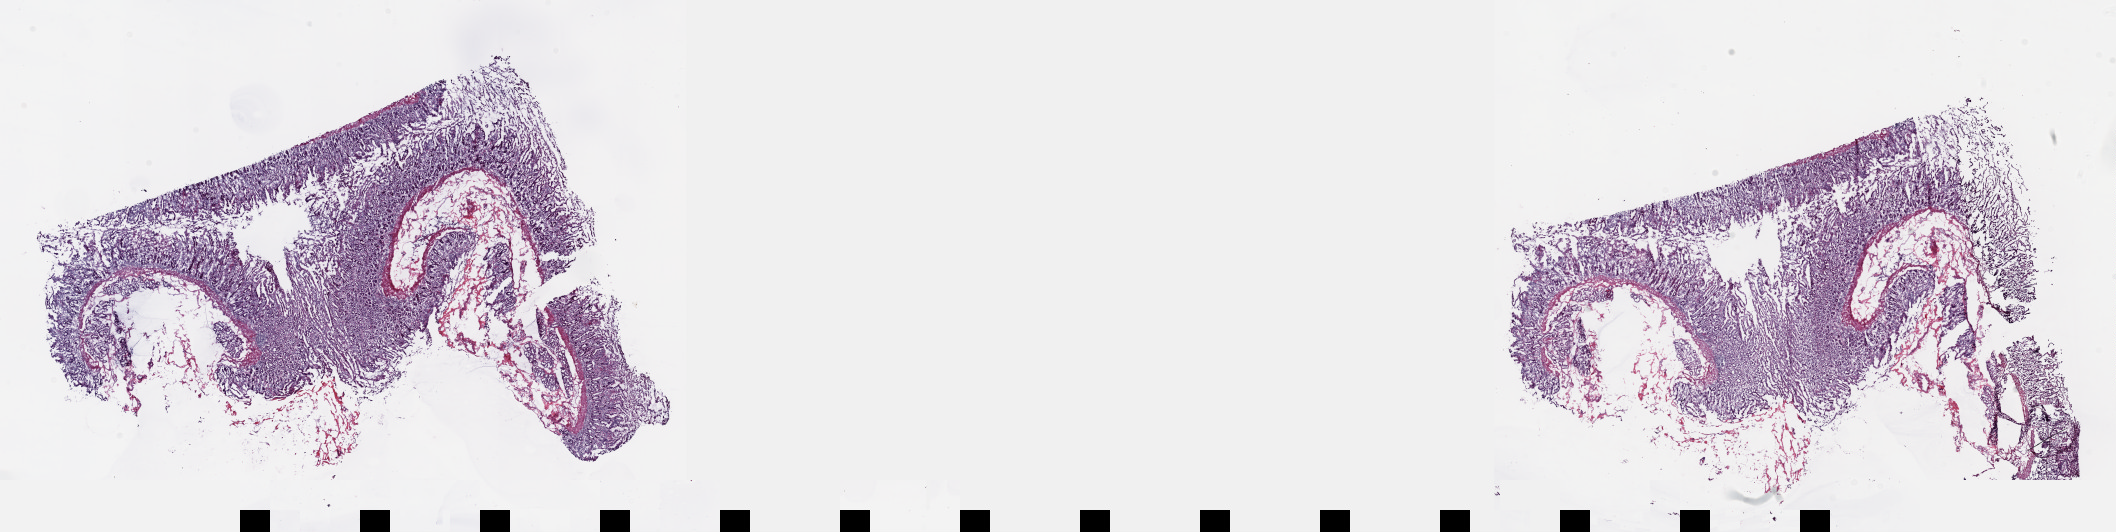
Hematoxylin and eosin (H&E) stained whole-slide image — low-resolution overview of the scanned area, about 34.1 x 8.6 mm, frozen section, sample: solid tissue normal (non-tumour tissue), pancreas. Male, age 54 years at initial diagnosis. Pathologist review of this section (percent, as recorded): tumour cells 0%, tumour nuclei 0%.
This section: solid tissue normal sample (biorepository sample class). Patient diagnosis: Infiltrating duct carcinoma, NOS (head of pancreas).